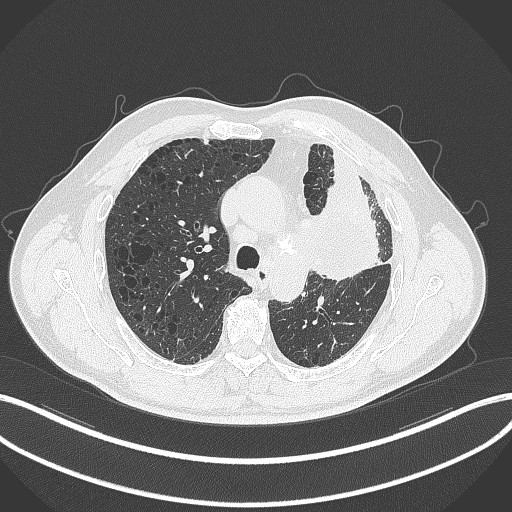
Chest CT, one axial slice; slice 214 of 297 in the series (ordered by position); reconstruction kernel B70f; lung window (W 1500 / L -600 HU); 1 mm slice thickness; 512 × 512 image matrix. Patient: male, 68 years. Case-level facts recorded for this patient, not image findings: clinical TNM (as recorded): T3 N3 M1.
Annotated regions visible in this slice (bounding box drawn by a radiologist):
- lung tumour (recorded histology: adenocarcinoma): bounding box <312,175,383,287> (left, top, right, bottom; pixels)